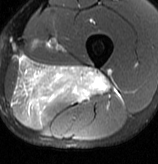
MRI of an extremity soft-tissue mass, one axial slice; position 35 of 70 along the scan axis; T2-weighted fat-saturated; MR volume resampled by the dataset authors to the PET/CT grid (not the native acquisition matrix); 3.27 mm slice thickness; 158 × 164 image matrix. Male patient. From the clinical record (not read from this slice): histological type: extraskeletal osteosarcoma; grade: high; site of the primary tumour: left adductur.
Structures marked on this image (expert contour drawn on MRI and transferred to this co-registered scan by the dataset authors):
- gross tumour volume (mass): bounding box <13,55,112,118> (left, top, right, bottom; pixels)